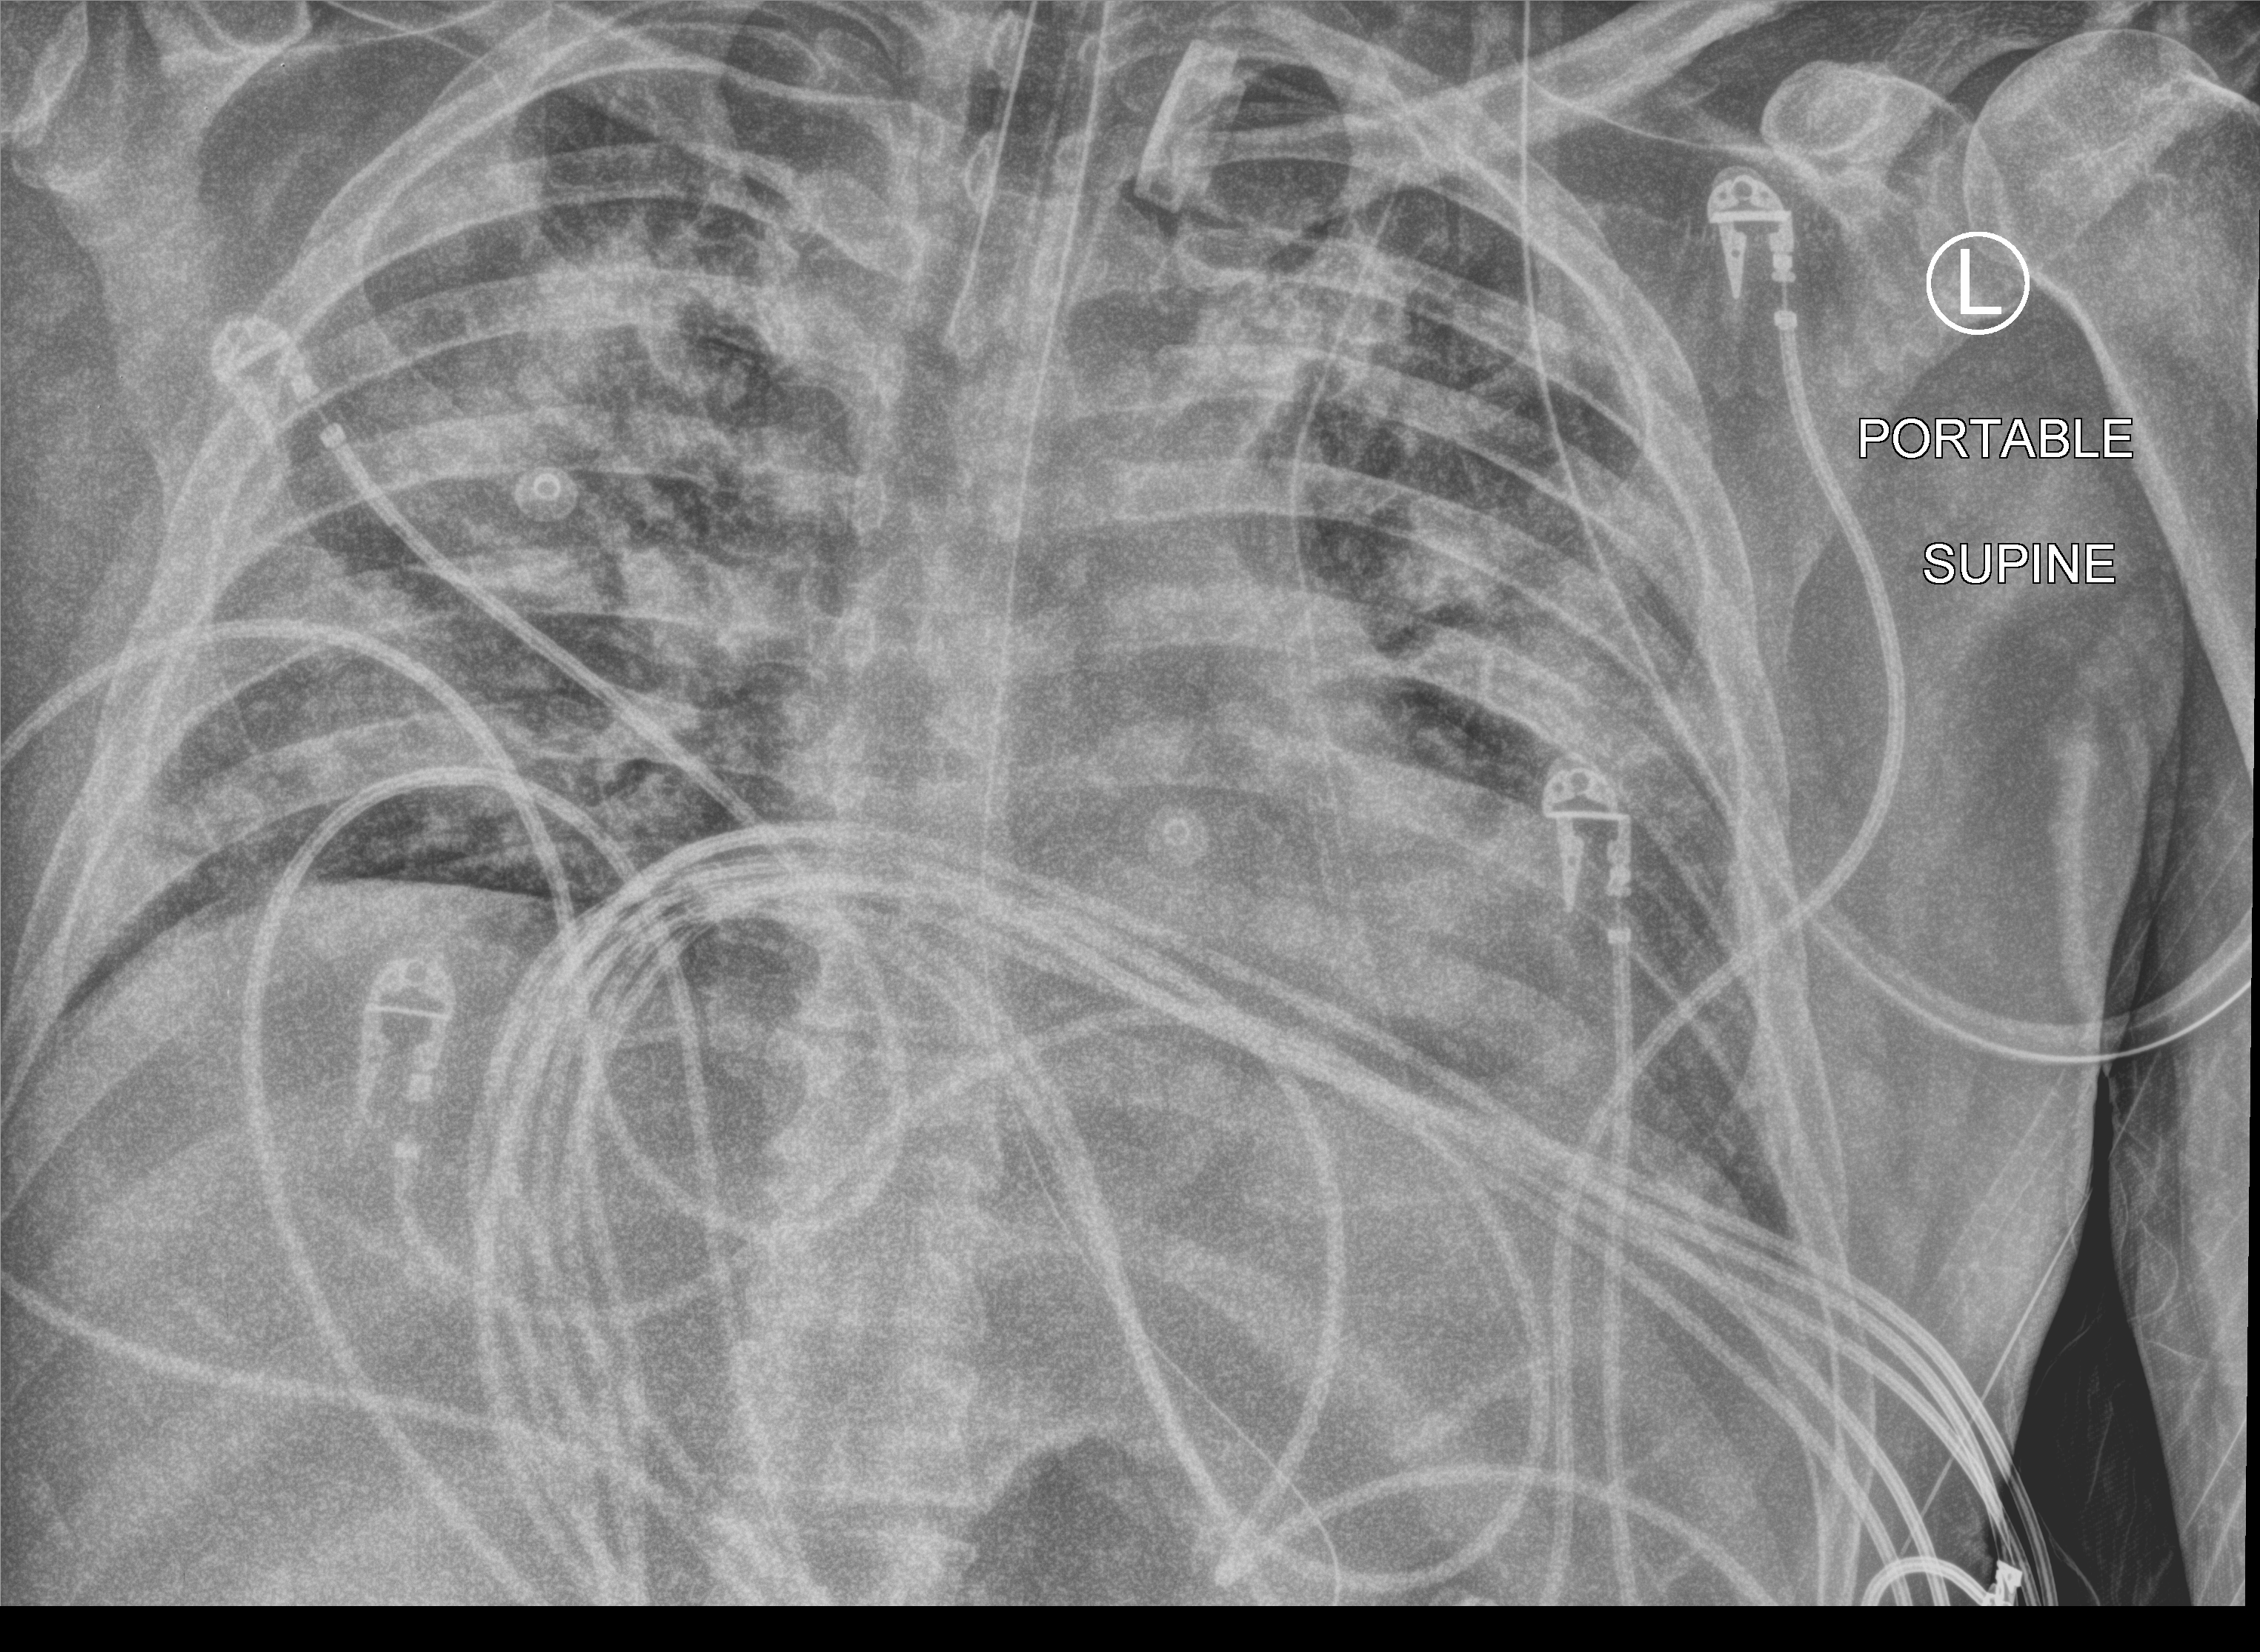
Portable chest radiograph; anteroposterior (AP) projection. Male patient hospitalised with COVID-19, age 18–59 years.
Admission-level facts for this patient (not findings on this image; timing relative to this image not recorded):
- admitted to intensive care during this hospital stay: yes
- mechanically ventilated during this hospital stay: yes
- length of hospital stay: 30 days